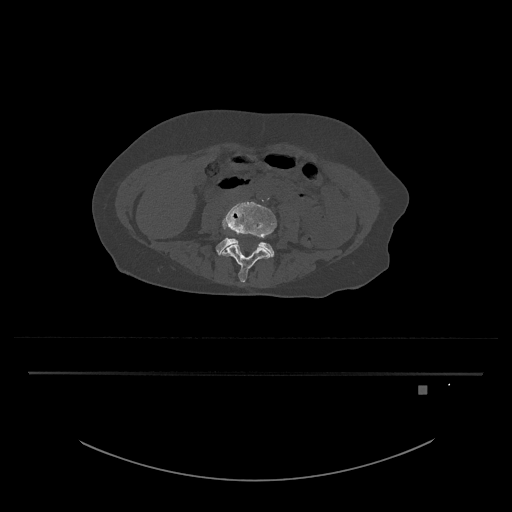
CT including the spine, one axial slice; position 342 of 797 along the scan axis; reconstruction kernel Br40s/3; 120 kVp; bone window (W 1800 / L 400 HU); 512 × 512 image matrix, field of view 500 × 500 mm. Patient: female, 57 years. From the clinical record (not read from this slice): primary cancer: cervical.
Outlined on this slice (semi-automatically segmented with operator editing):
- L4 vertebra: box from (x=220, y=202) to (x=277, y=283) px